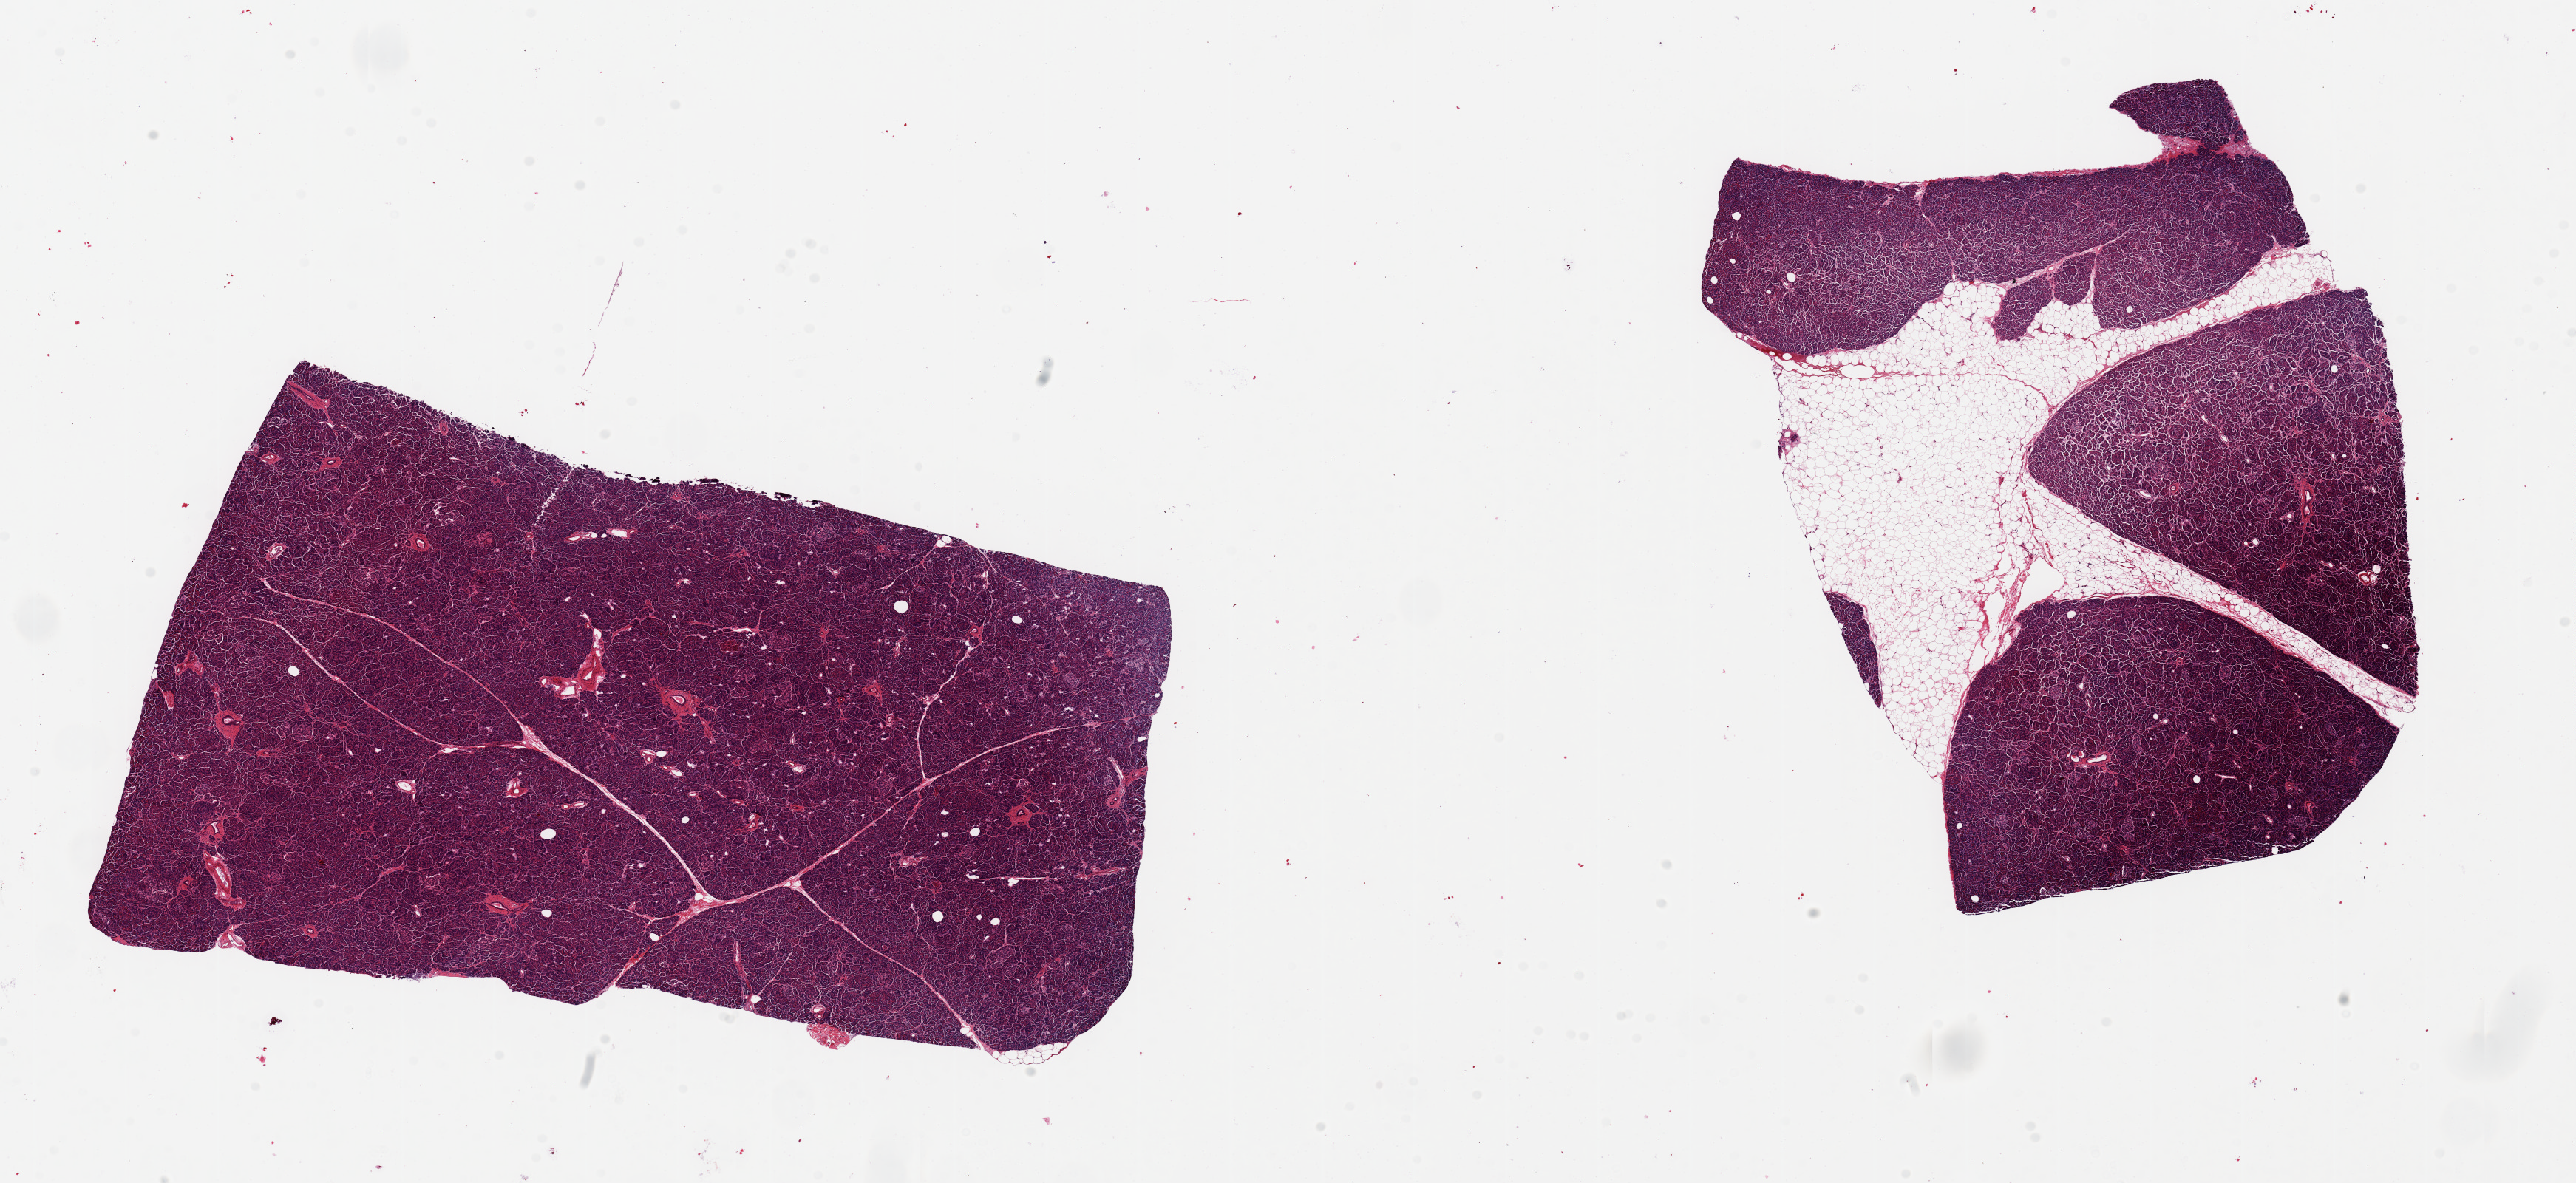
Whole-slide image, haematoxylin and eosin stain, whole scanned area (about 27.6 x 12.7 mm) shown as a low-resolution overview, PAXgene-fixed, paraffin-embedded tissue, target tissue: pancreas, donor tissue sample. Male donor.
Review note (as recorded): 2 pieces, 11x6.5 & 8.5x7mm; 1 piece with ~40% internal adipose, other without adipose.